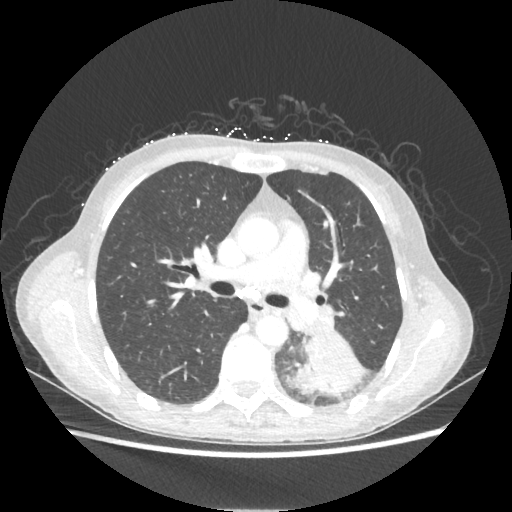
Chest CT, one axial slice. Position 129 of 221 along the scan axis. Lung window (W 1500 / L -600 HU). 1.25 mm slice thickness. 512 × 512 image matrix, field of view 360 × 360 mm. Patient: female, 53 years. From the clinical record (not read from this slice): clinical TNM (as recorded): T3 N0 M0.
Annotated regions visible in this slice (rectangle marked by the reading radiologist):
- lung tumour (recorded histology: adenocarcinoma): bounding box <292,332,365,398> (left, top, right, bottom; pixels)